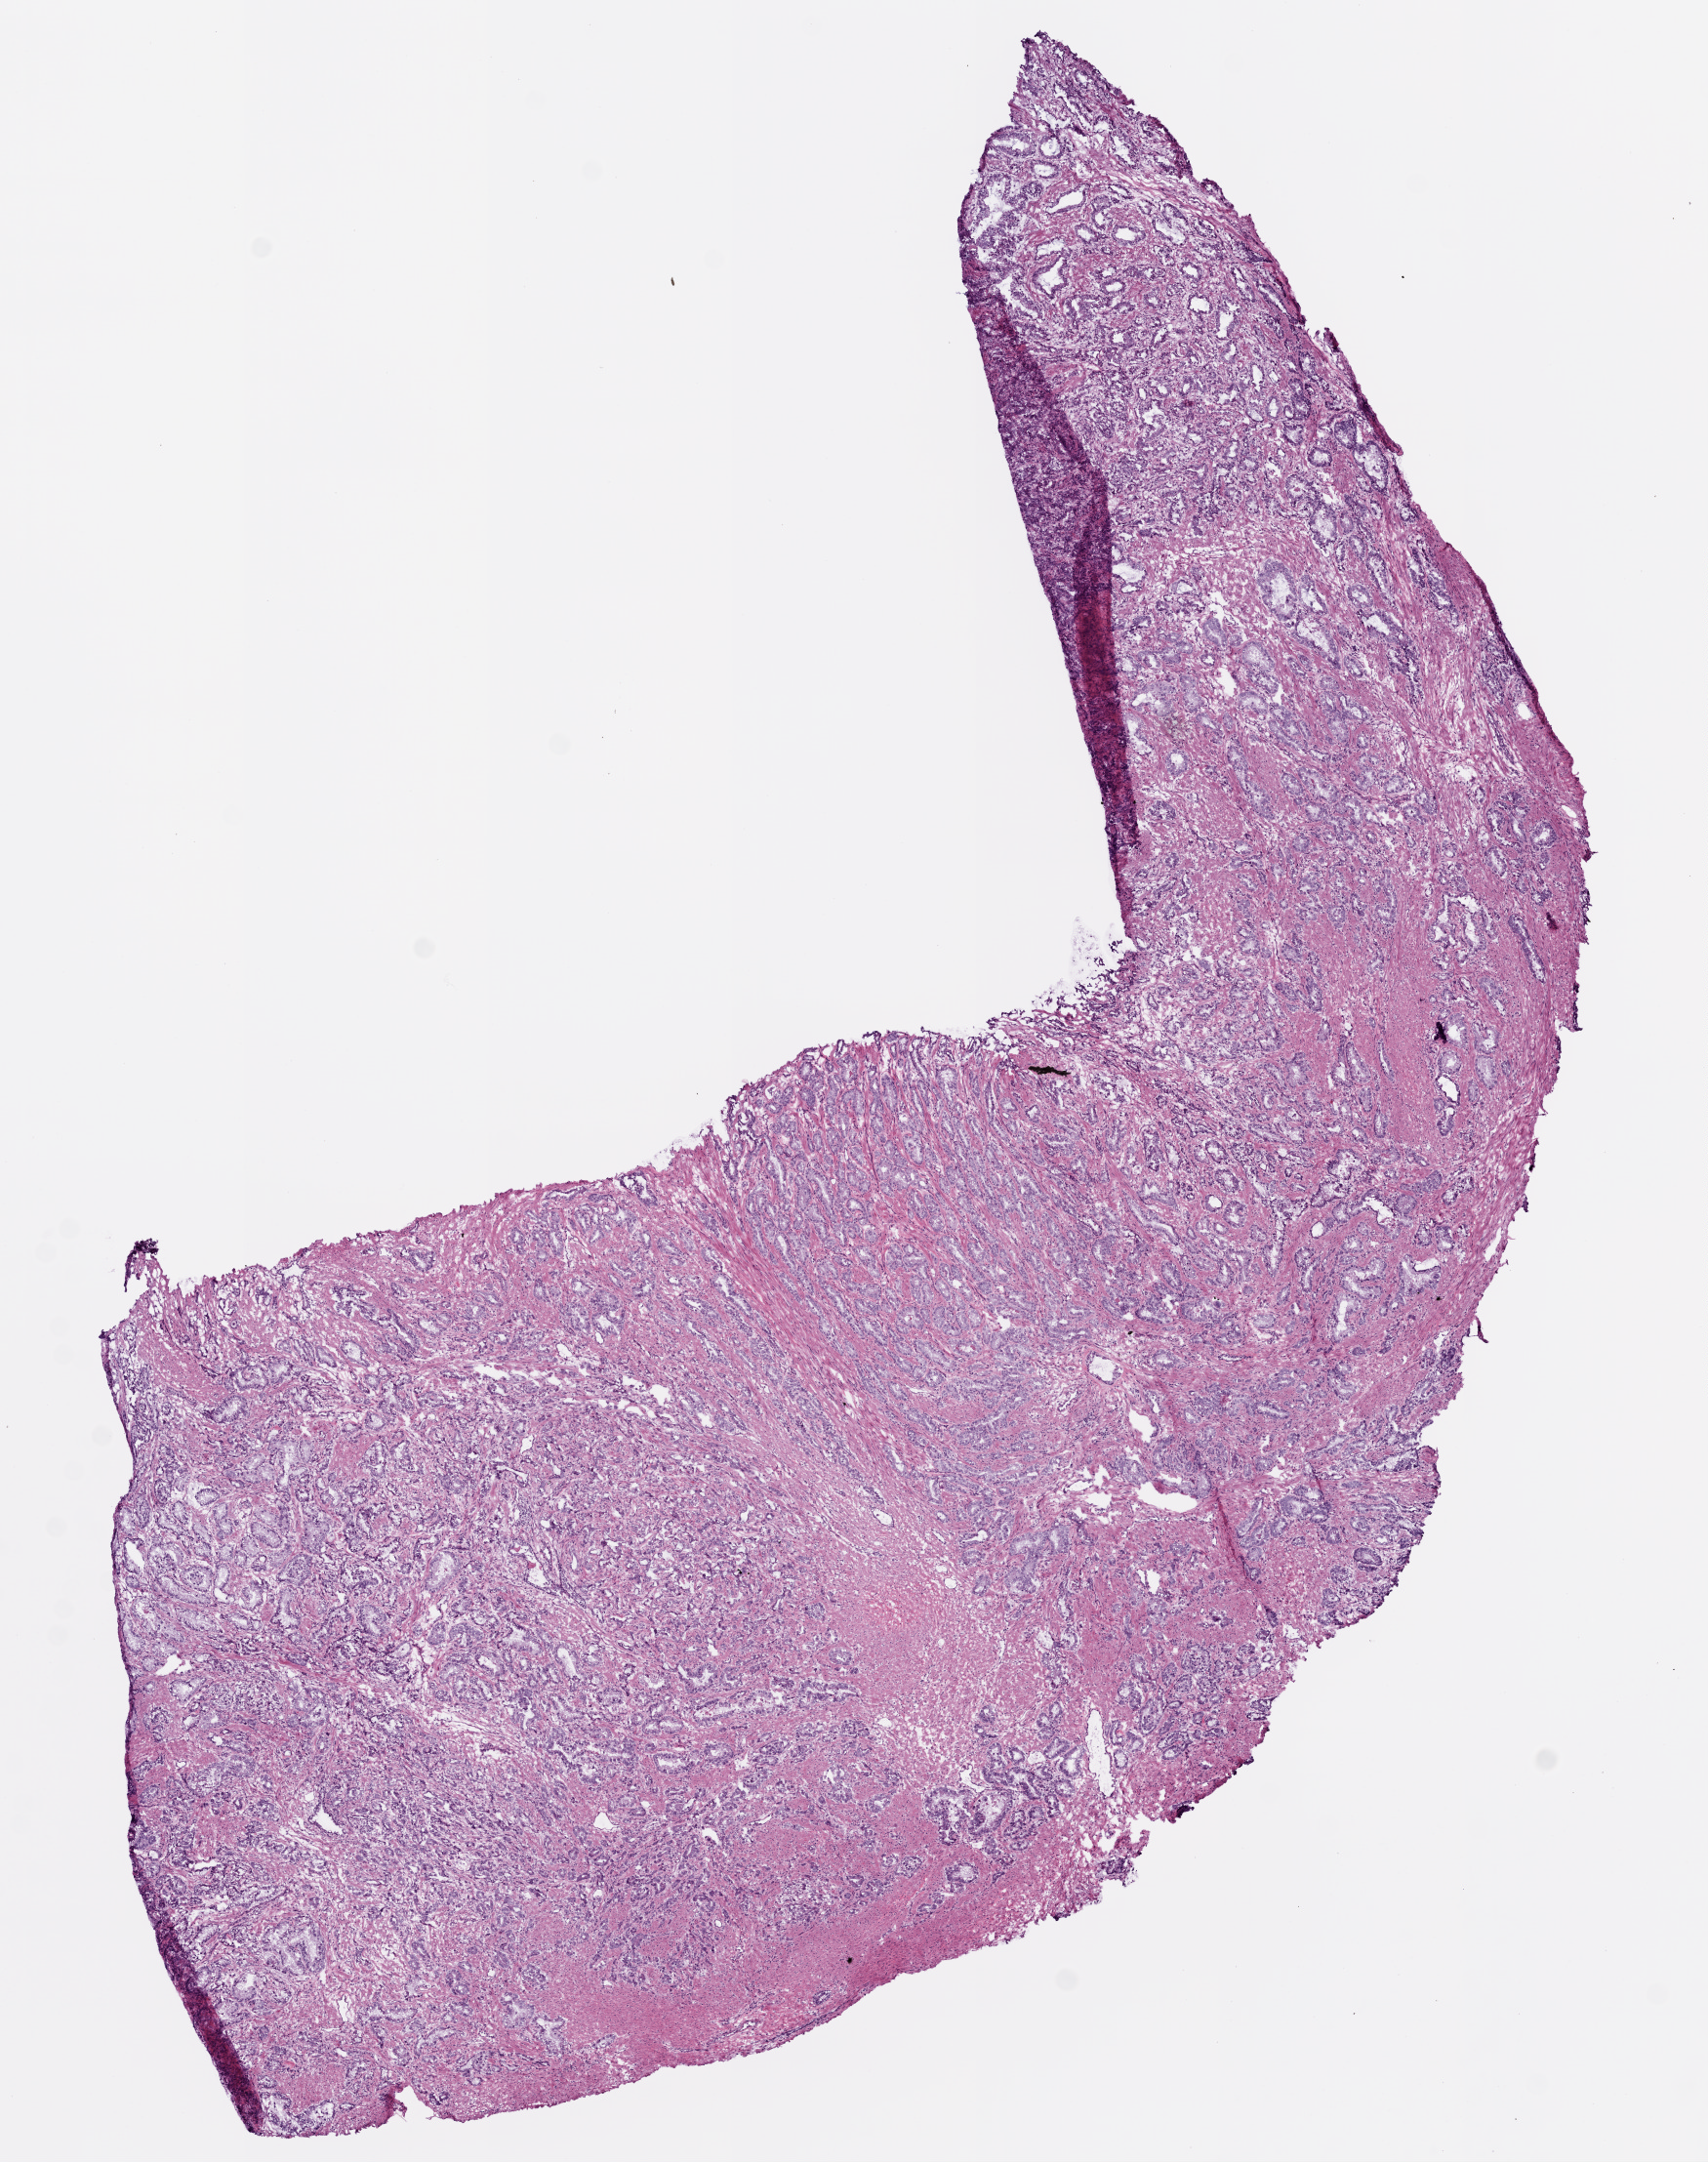
H&E-stained whole-slide image — a low-resolution overview of the entire scanned area, about 7.0 x 8.9 mm. Frozen section from the bottom of the tissue portion. Sample: primary tumour, prostate. Male, age 63 years at initial diagnosis. Gleason score: 9 (4+5). Slide review estimates, as recorded: tumour cells 60%, tumour nuclei 70%, normal cells 25%, stromal cells 15%, necrosis 0%. Infiltration values recorded for this section: lymphocyte infiltration 0%, monocyte infiltration 0%, neutrophil infiltration 0%.
Laterality: bilateral. Diagnosis: Acinar cell carcinoma (prostate gland). Lymph nodes positive (case pathology): 0 of 6 examined.